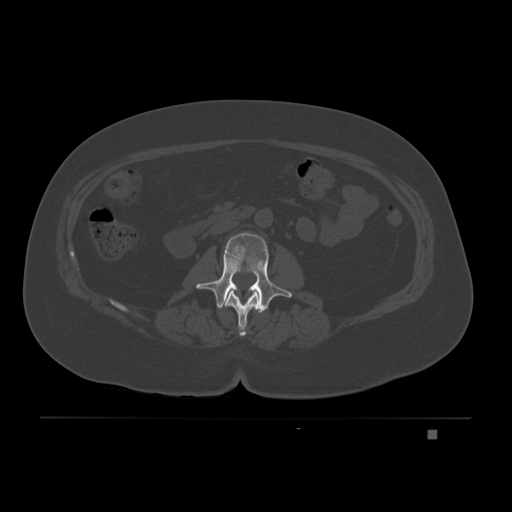
CT including the spine, one axial slice. Slice 63 of 221 in the series (ordered by position). Bone window (W 1800 / L 400 HU). 3 mm slice thickness. 512 × 512 image matrix, field of view 474 × 474 mm. Patient: female, 63 years. Case-level facts recorded for this patient, not image findings: primary cancer: breast.
Outlined on this slice (semi-automatically segmented with operator editing):
- L1 vertebra: bounding box [x1, y1, x2, y2] px = [223, 289, 261, 336]
- L2 vertebra: [196, 232, 292, 312]